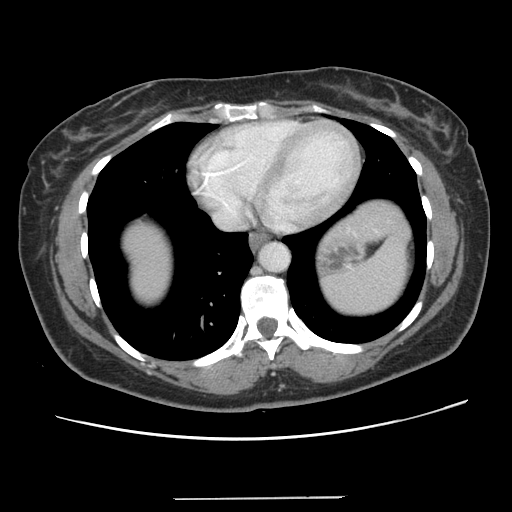
Contrast-enhanced abdominal CT, one axial slice. Slice 126 of 141 in the series (ordered by position). 120 kVp. Intravenous contrast given. Soft-tissue window (W 400 / L 40 HU). 2.5 mm slice thickness. 512 × 512 image matrix, field of view 366 × 366 mm. Female patient, age 53 years. From the clinical record (not read from this slice): diagnosis: colorectal cancer liver metastases, imaged before liver resection.
Structures marked on this image (outlined manually by an expert reader):
- liver: bounding box (x1, y1, x2, y2) in pixels: (121, 200, 402, 306)
- planned liver remnant (the part of the liver to remain after resection): (121, 222, 174, 308)